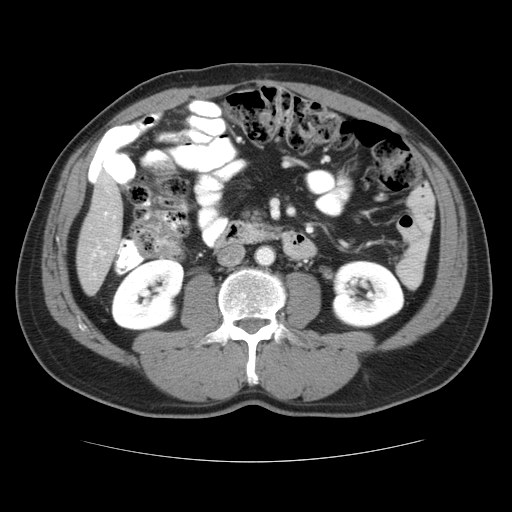
Contrast-enhanced abdominal CT, one axial slice. Position 10 of 37 along the scan axis. 120 kVp. Intravenous contrast given. Soft-tissue window (W 400 / L 40 HU). 512 × 512 image matrix. Male patient, age 66 years. Case-level facts recorded for this patient, not image findings: diagnosis: colorectal cancer liver metastases, imaged before liver resection; multiple liver metastases: yes; largest metastasis: 1.6 cm; disease in both lobes: yes.
Structures marked on this image (expert manual segmentation):
- hepatic veins: bounding box (x1, y1, x2, y2) in pixels: (92, 211, 116, 257)
- liver: (77, 169, 125, 294)
- planned liver remnant (the part of the liver to remain after resection): (77, 172, 125, 295)
- liver metastasis: (100, 228, 107, 235)